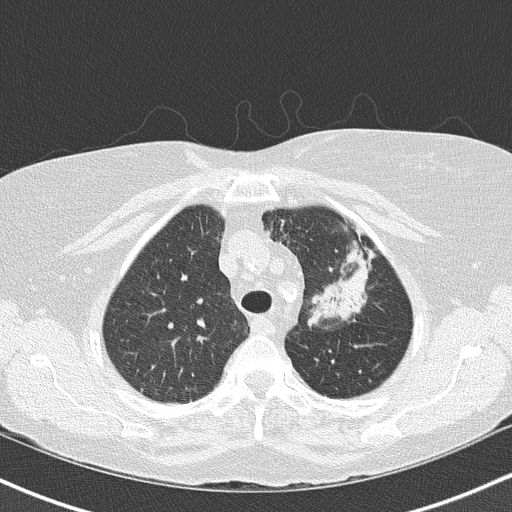
Low-dose screening chest CT, one axial slice. Position 118 of 147 along the scan axis. Lung window (W 1500 / L -600 HU). 2 mm slice thickness. 512 × 512 image matrix, field of view 320 × 320 mm.
Structures marked on this image (expert manual segmentation):
- lesion 1 (tumor, upper lobe of left lung): bounding box <310,263,369,323> (left, top, right, bottom; pixels)